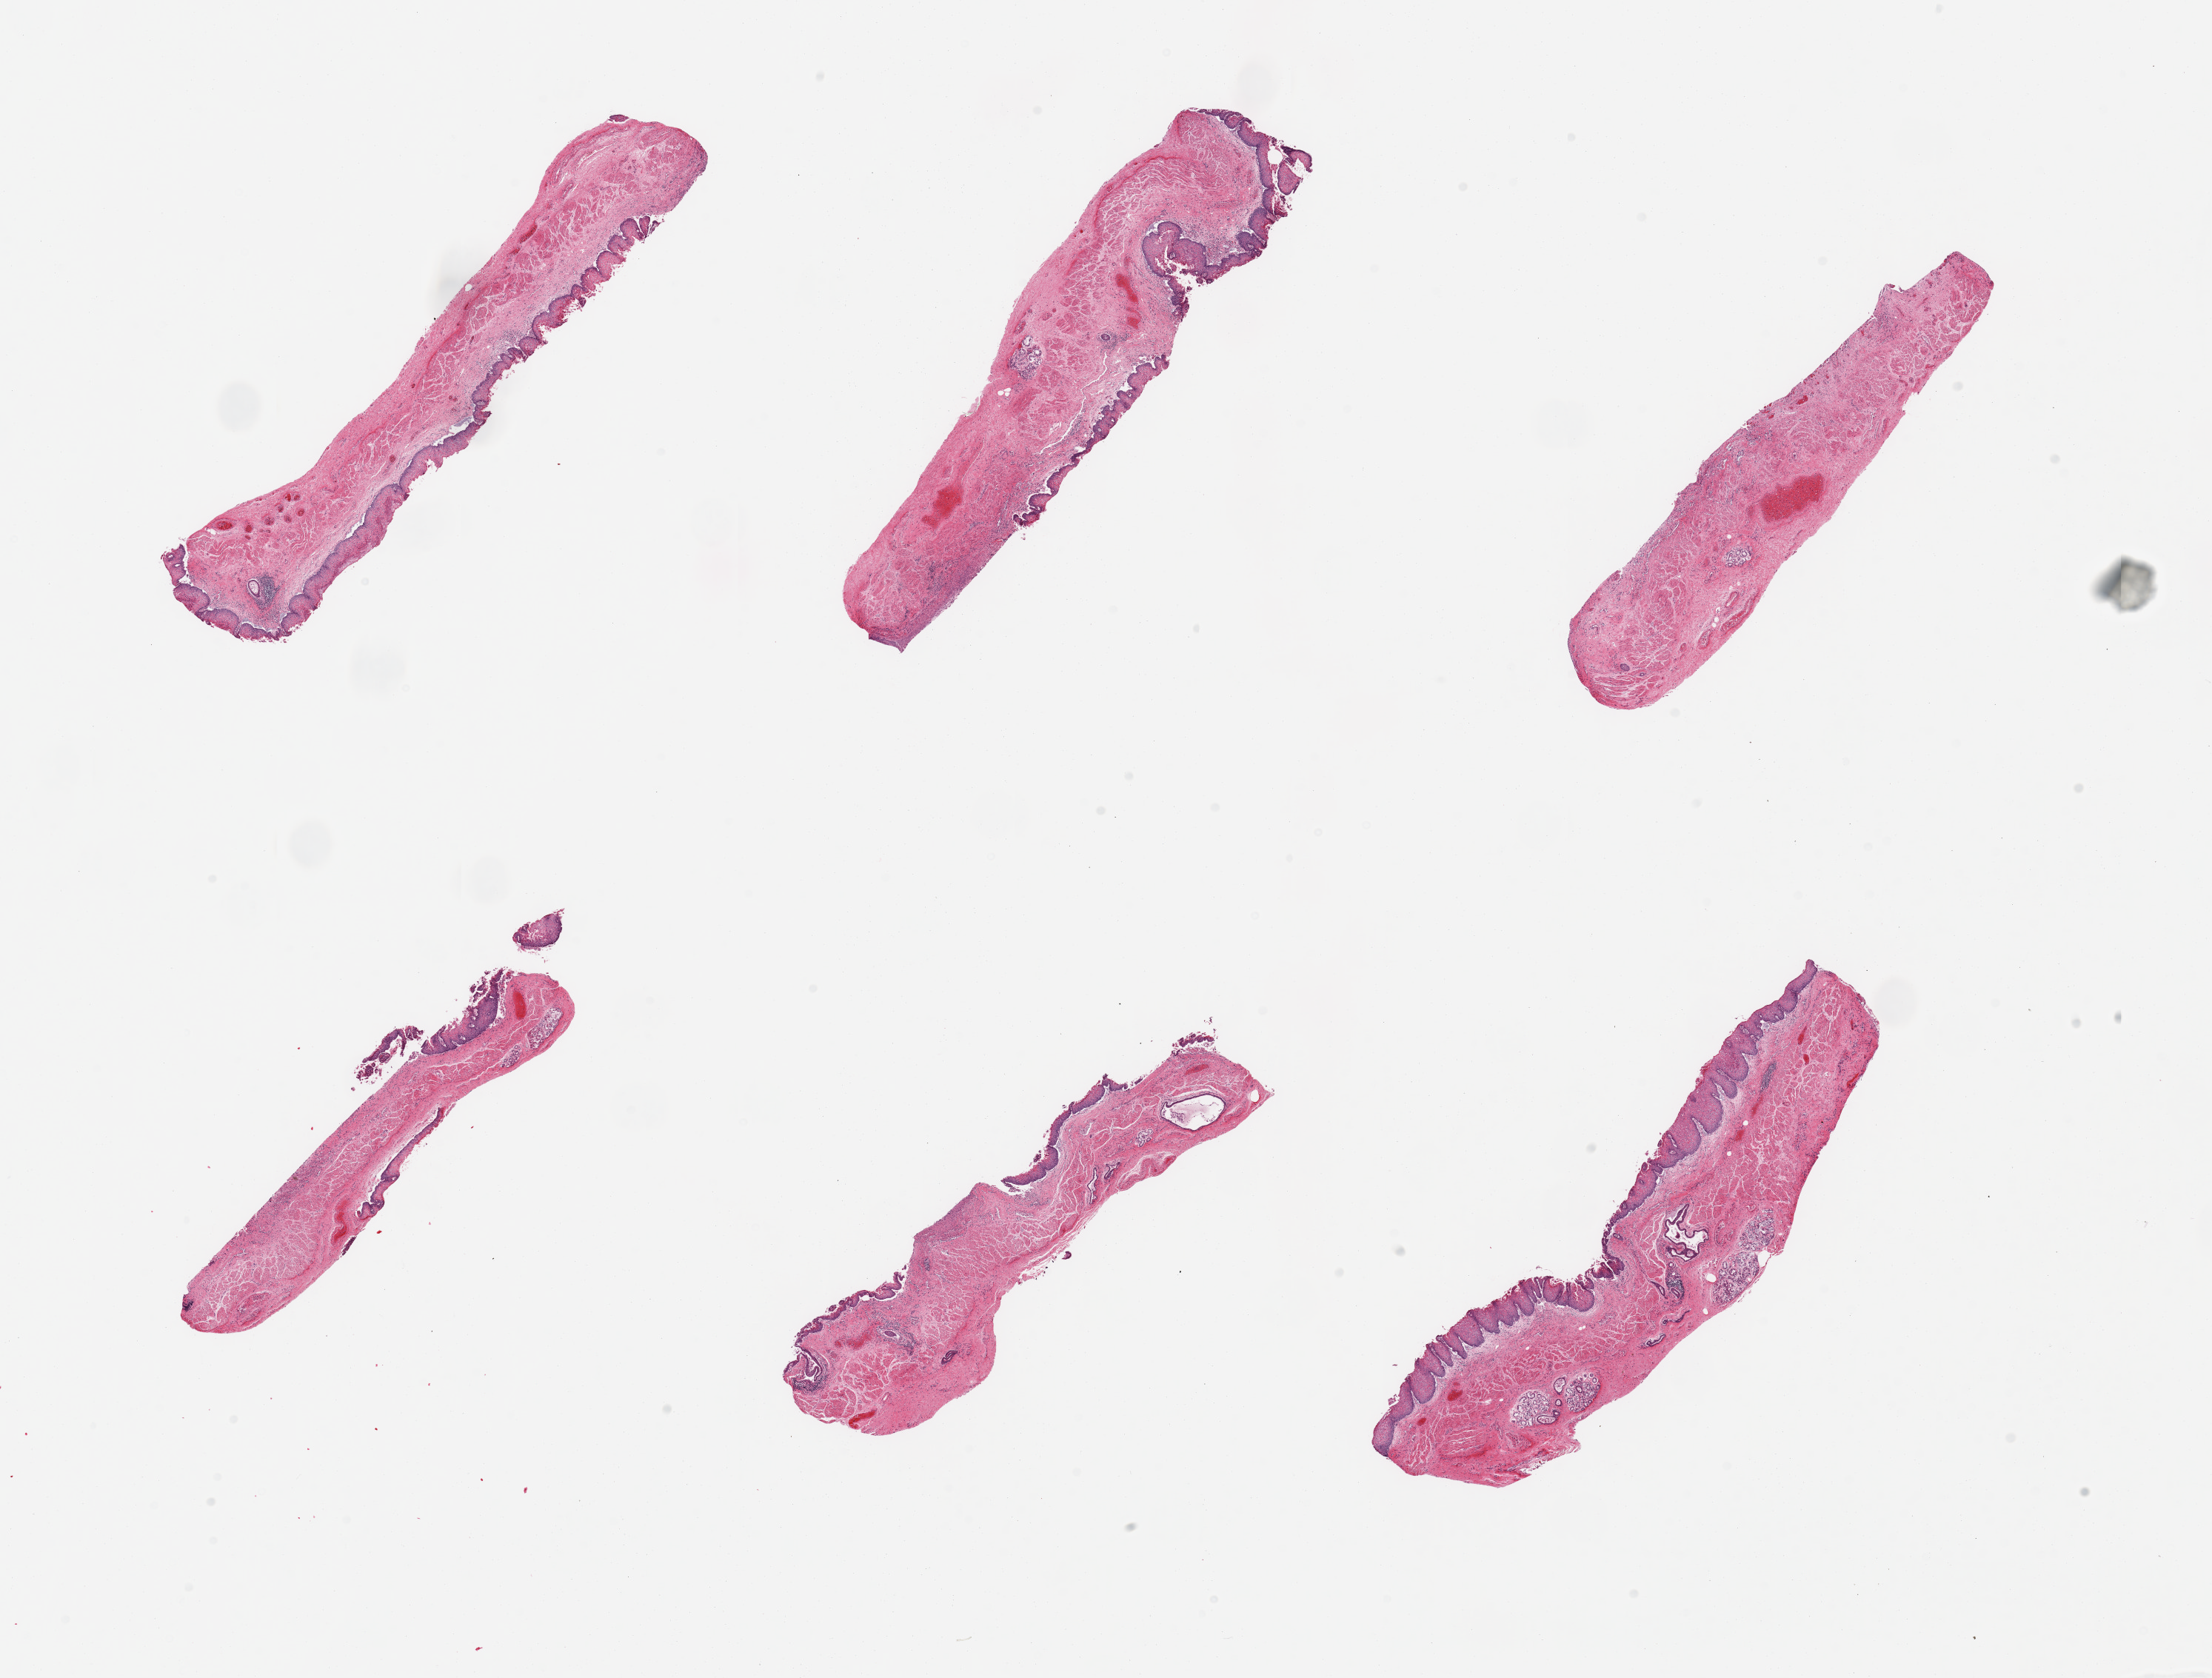
Digitized haematoxylin and eosin-stained section, whole scanned area (about 23.6 x 17.9 mm) shown as a low-resolution overview. PAXgene-fixed paraffin-embedded (PFPE) section. Target tissue: esophageal mucous membrane. Donor tissue sample. Donor sex: male.
Review note (as recorded): 6 pieces; few dilated glands, squamous epithelium incomplete, focal ulceration.